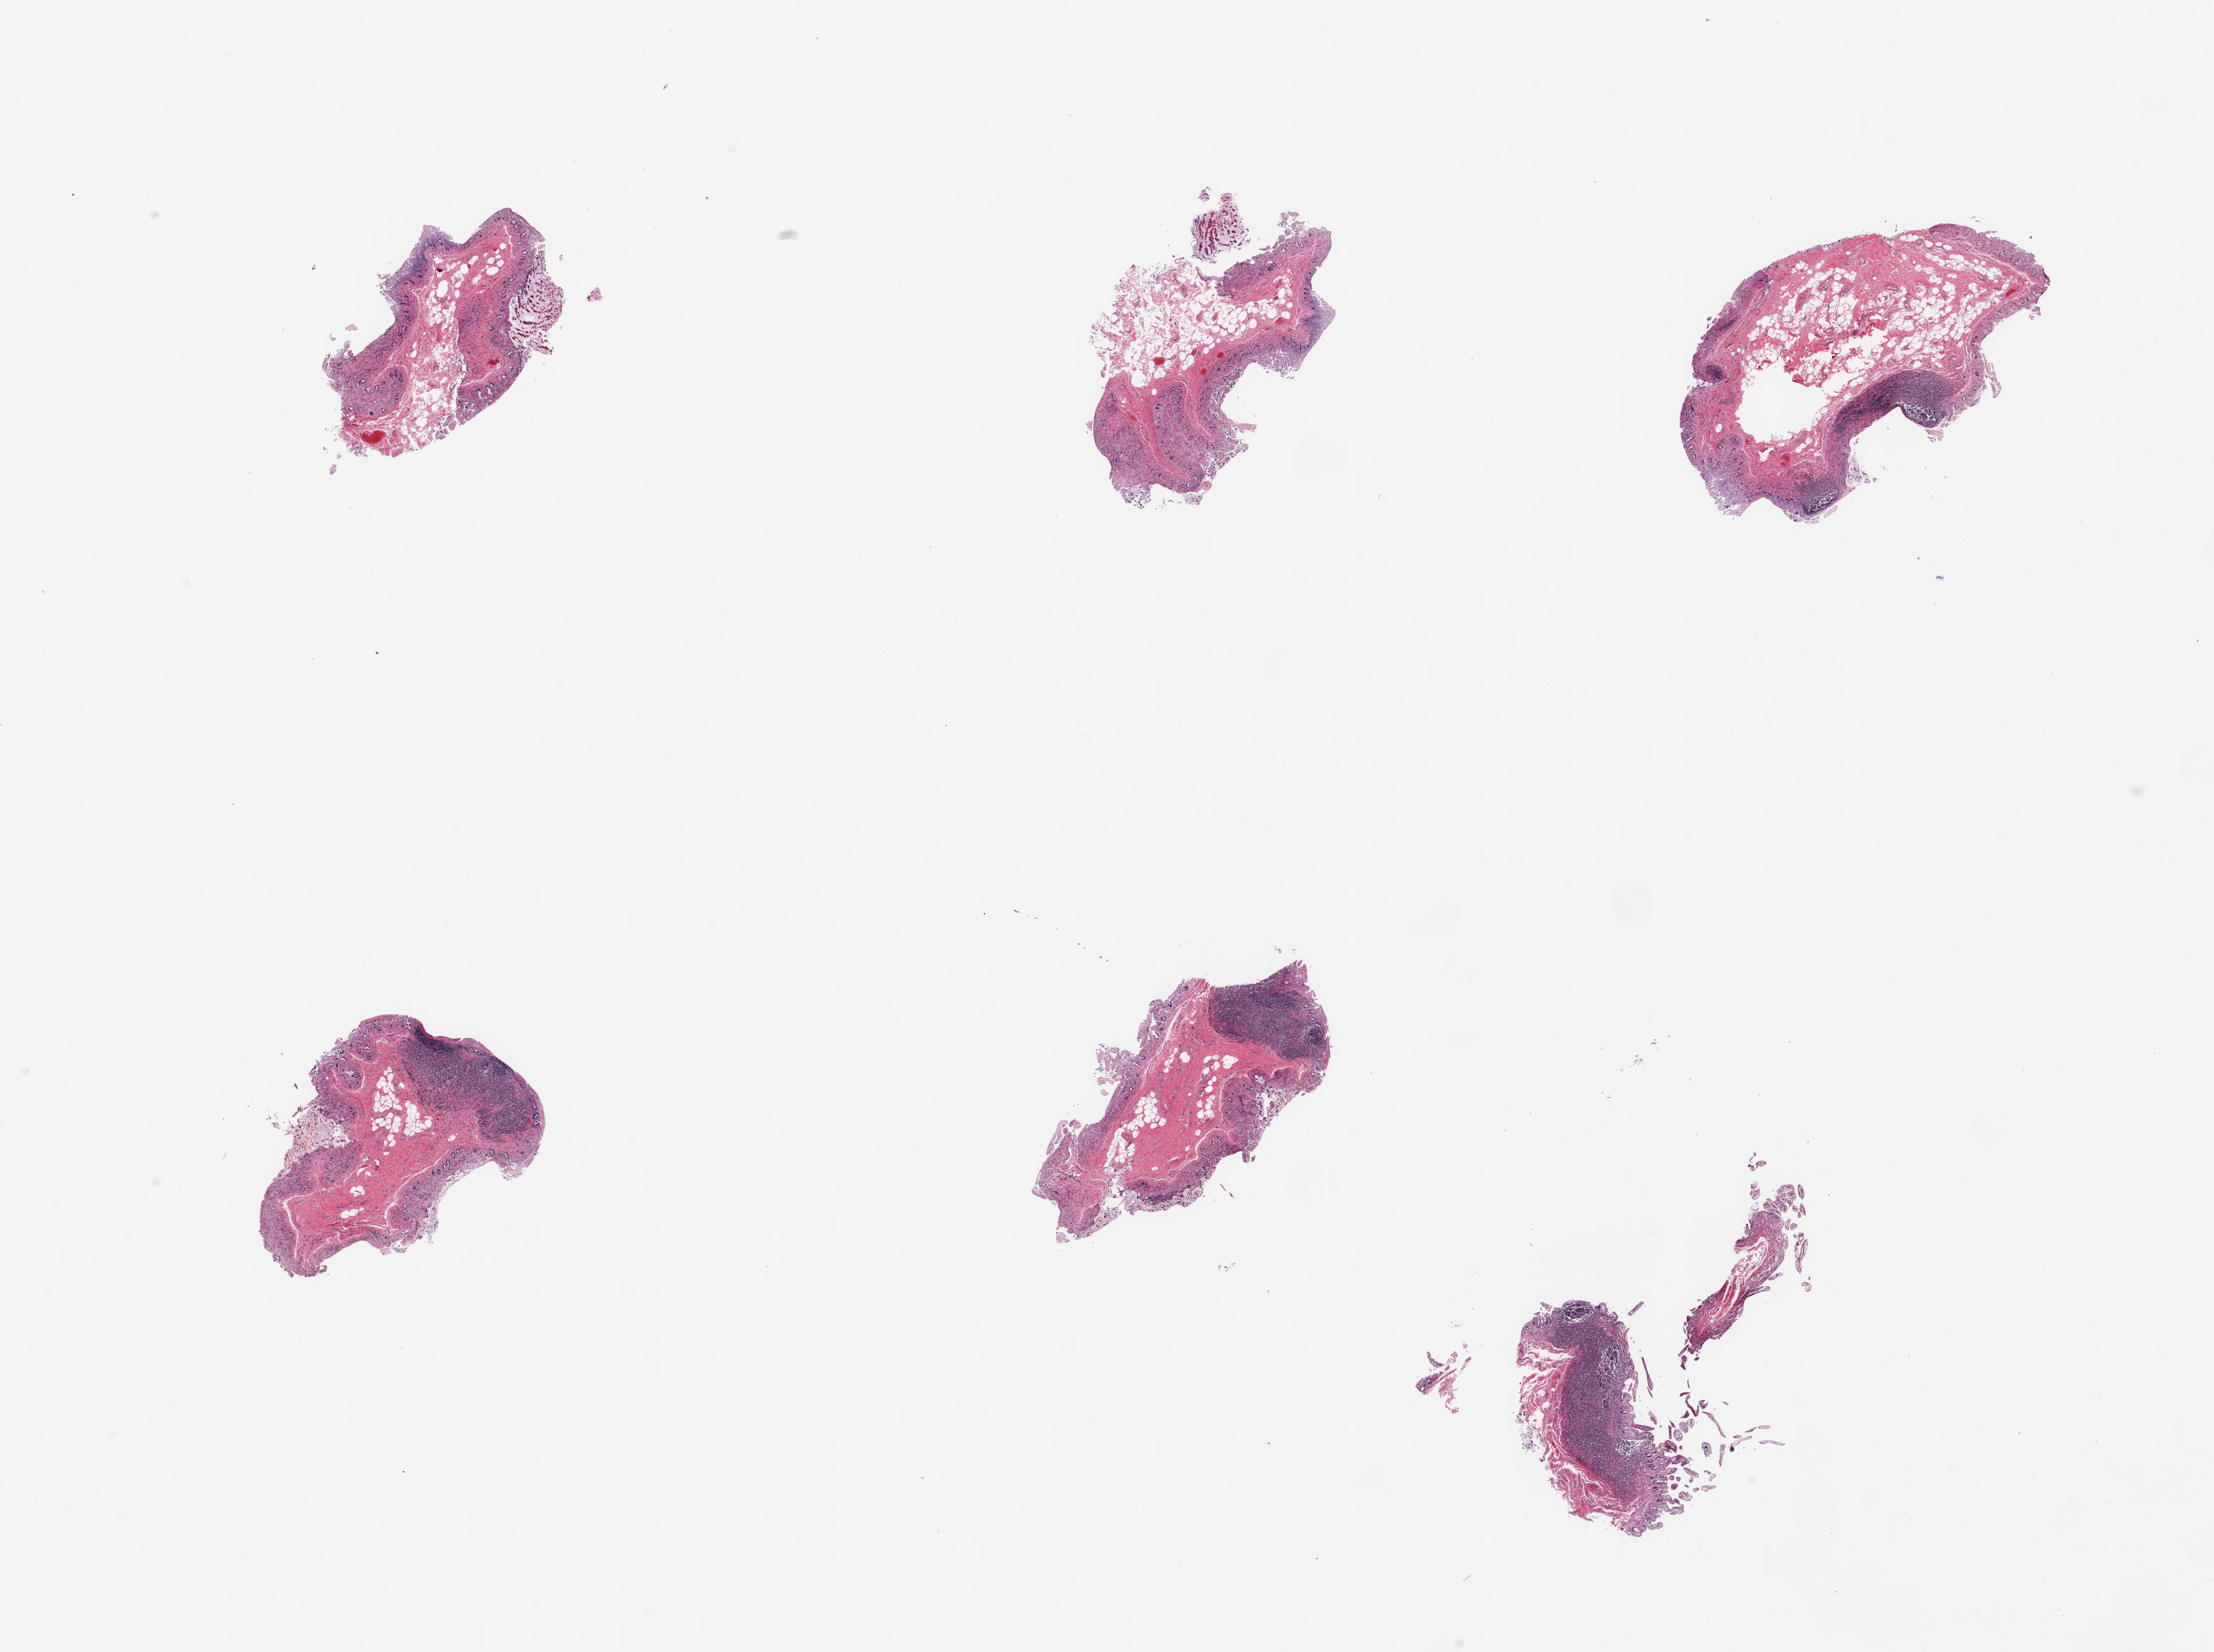
Whole-slide image, haematoxylin and eosin stain, shown as a low-resolution overview of the whole scanned area (about 24.6 x 18.4 mm, slide scanned at 20x). Donor sex: male.
• specimen: PAXgene-fixed paraffin-embedded (PFPE) section; target tissue: ileum; tissue donor sample